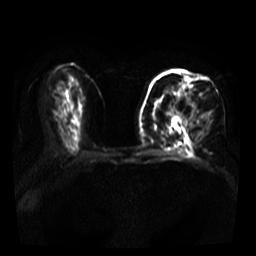
Breast MRI, one axial slice; position 19 of 39 along the scan axis; diffusion-weighted series; image 2 of 4 stored at this slice position (different b-values; order by instance number); 3 T; 5 mm slice thickness; 256 × 256 image matrix. Female patient.
Outlined on this slice (manually delineated by an expert):
- tumour on diffusion-weighted imaging: bounding box (x1, y1, x2, y2) in pixels: (155, 83, 211, 120)